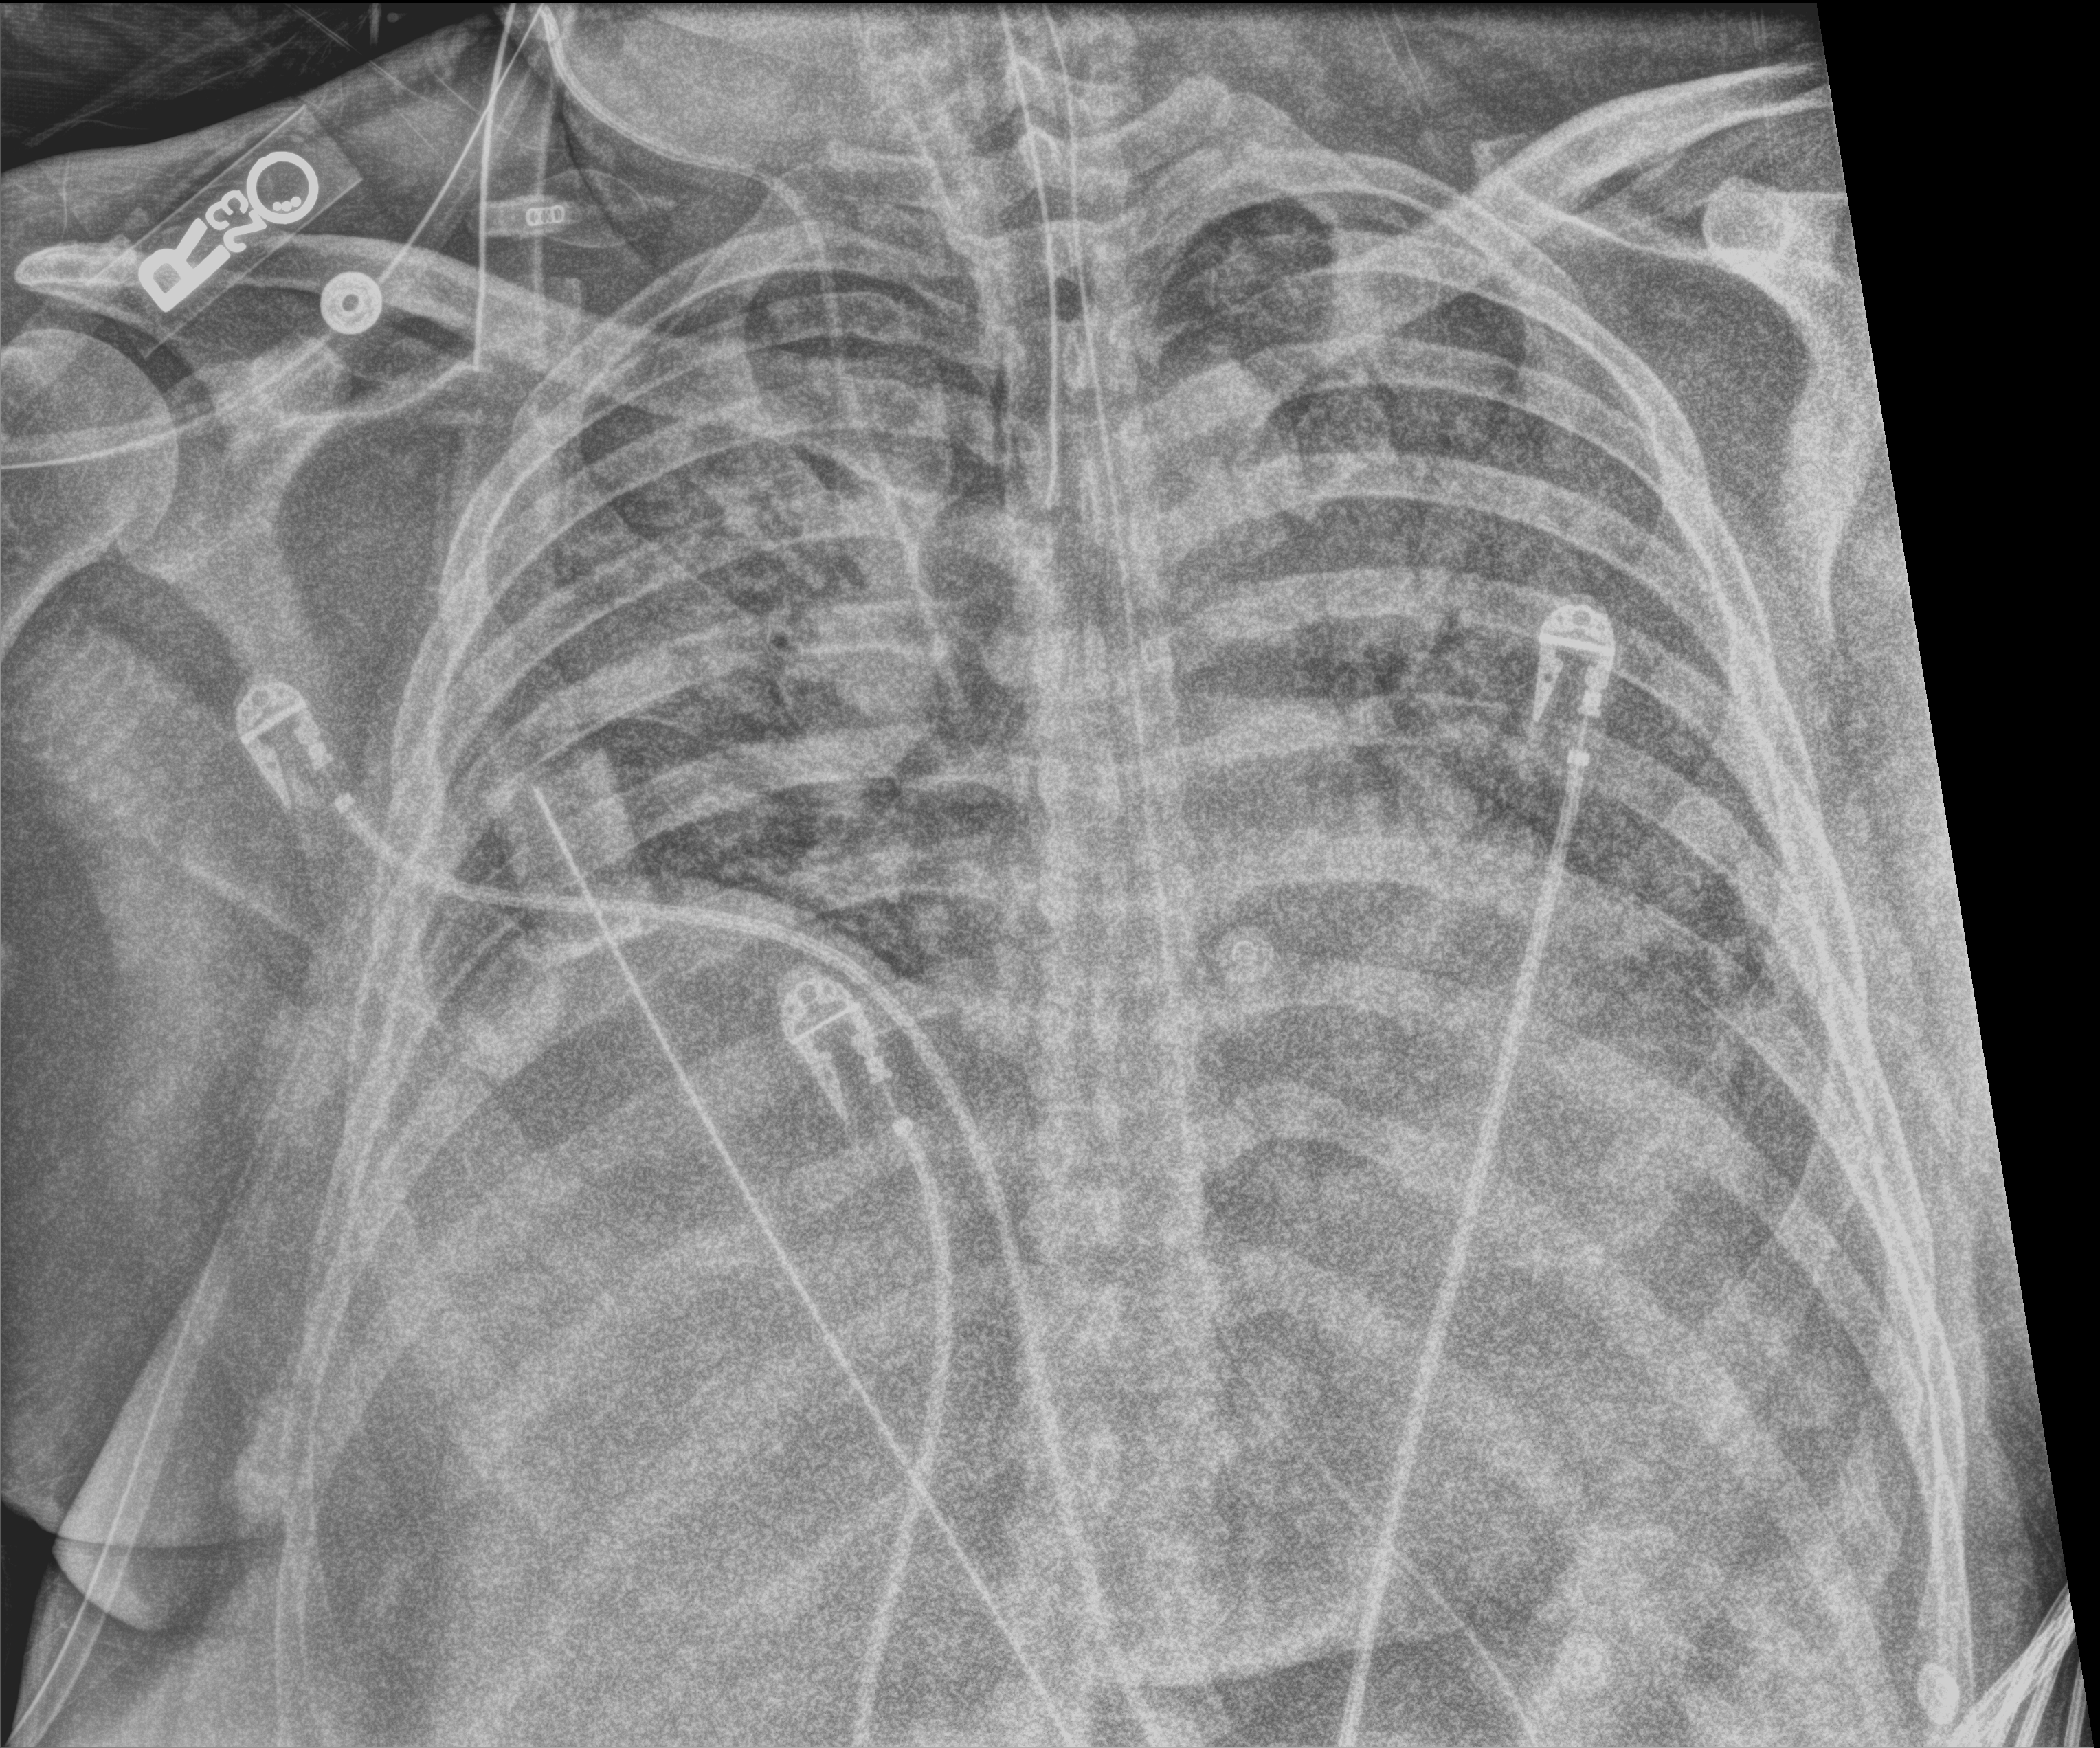
Portable chest radiograph, anteroposterior (AP) projection. Patient hospitalised with COVID-19; male, aged 18–59 years.
From the hospital-stay record, not from the radiograph (when in the stay this image was taken is not recorded): admitted to intensive care during this hospital stay: yes.